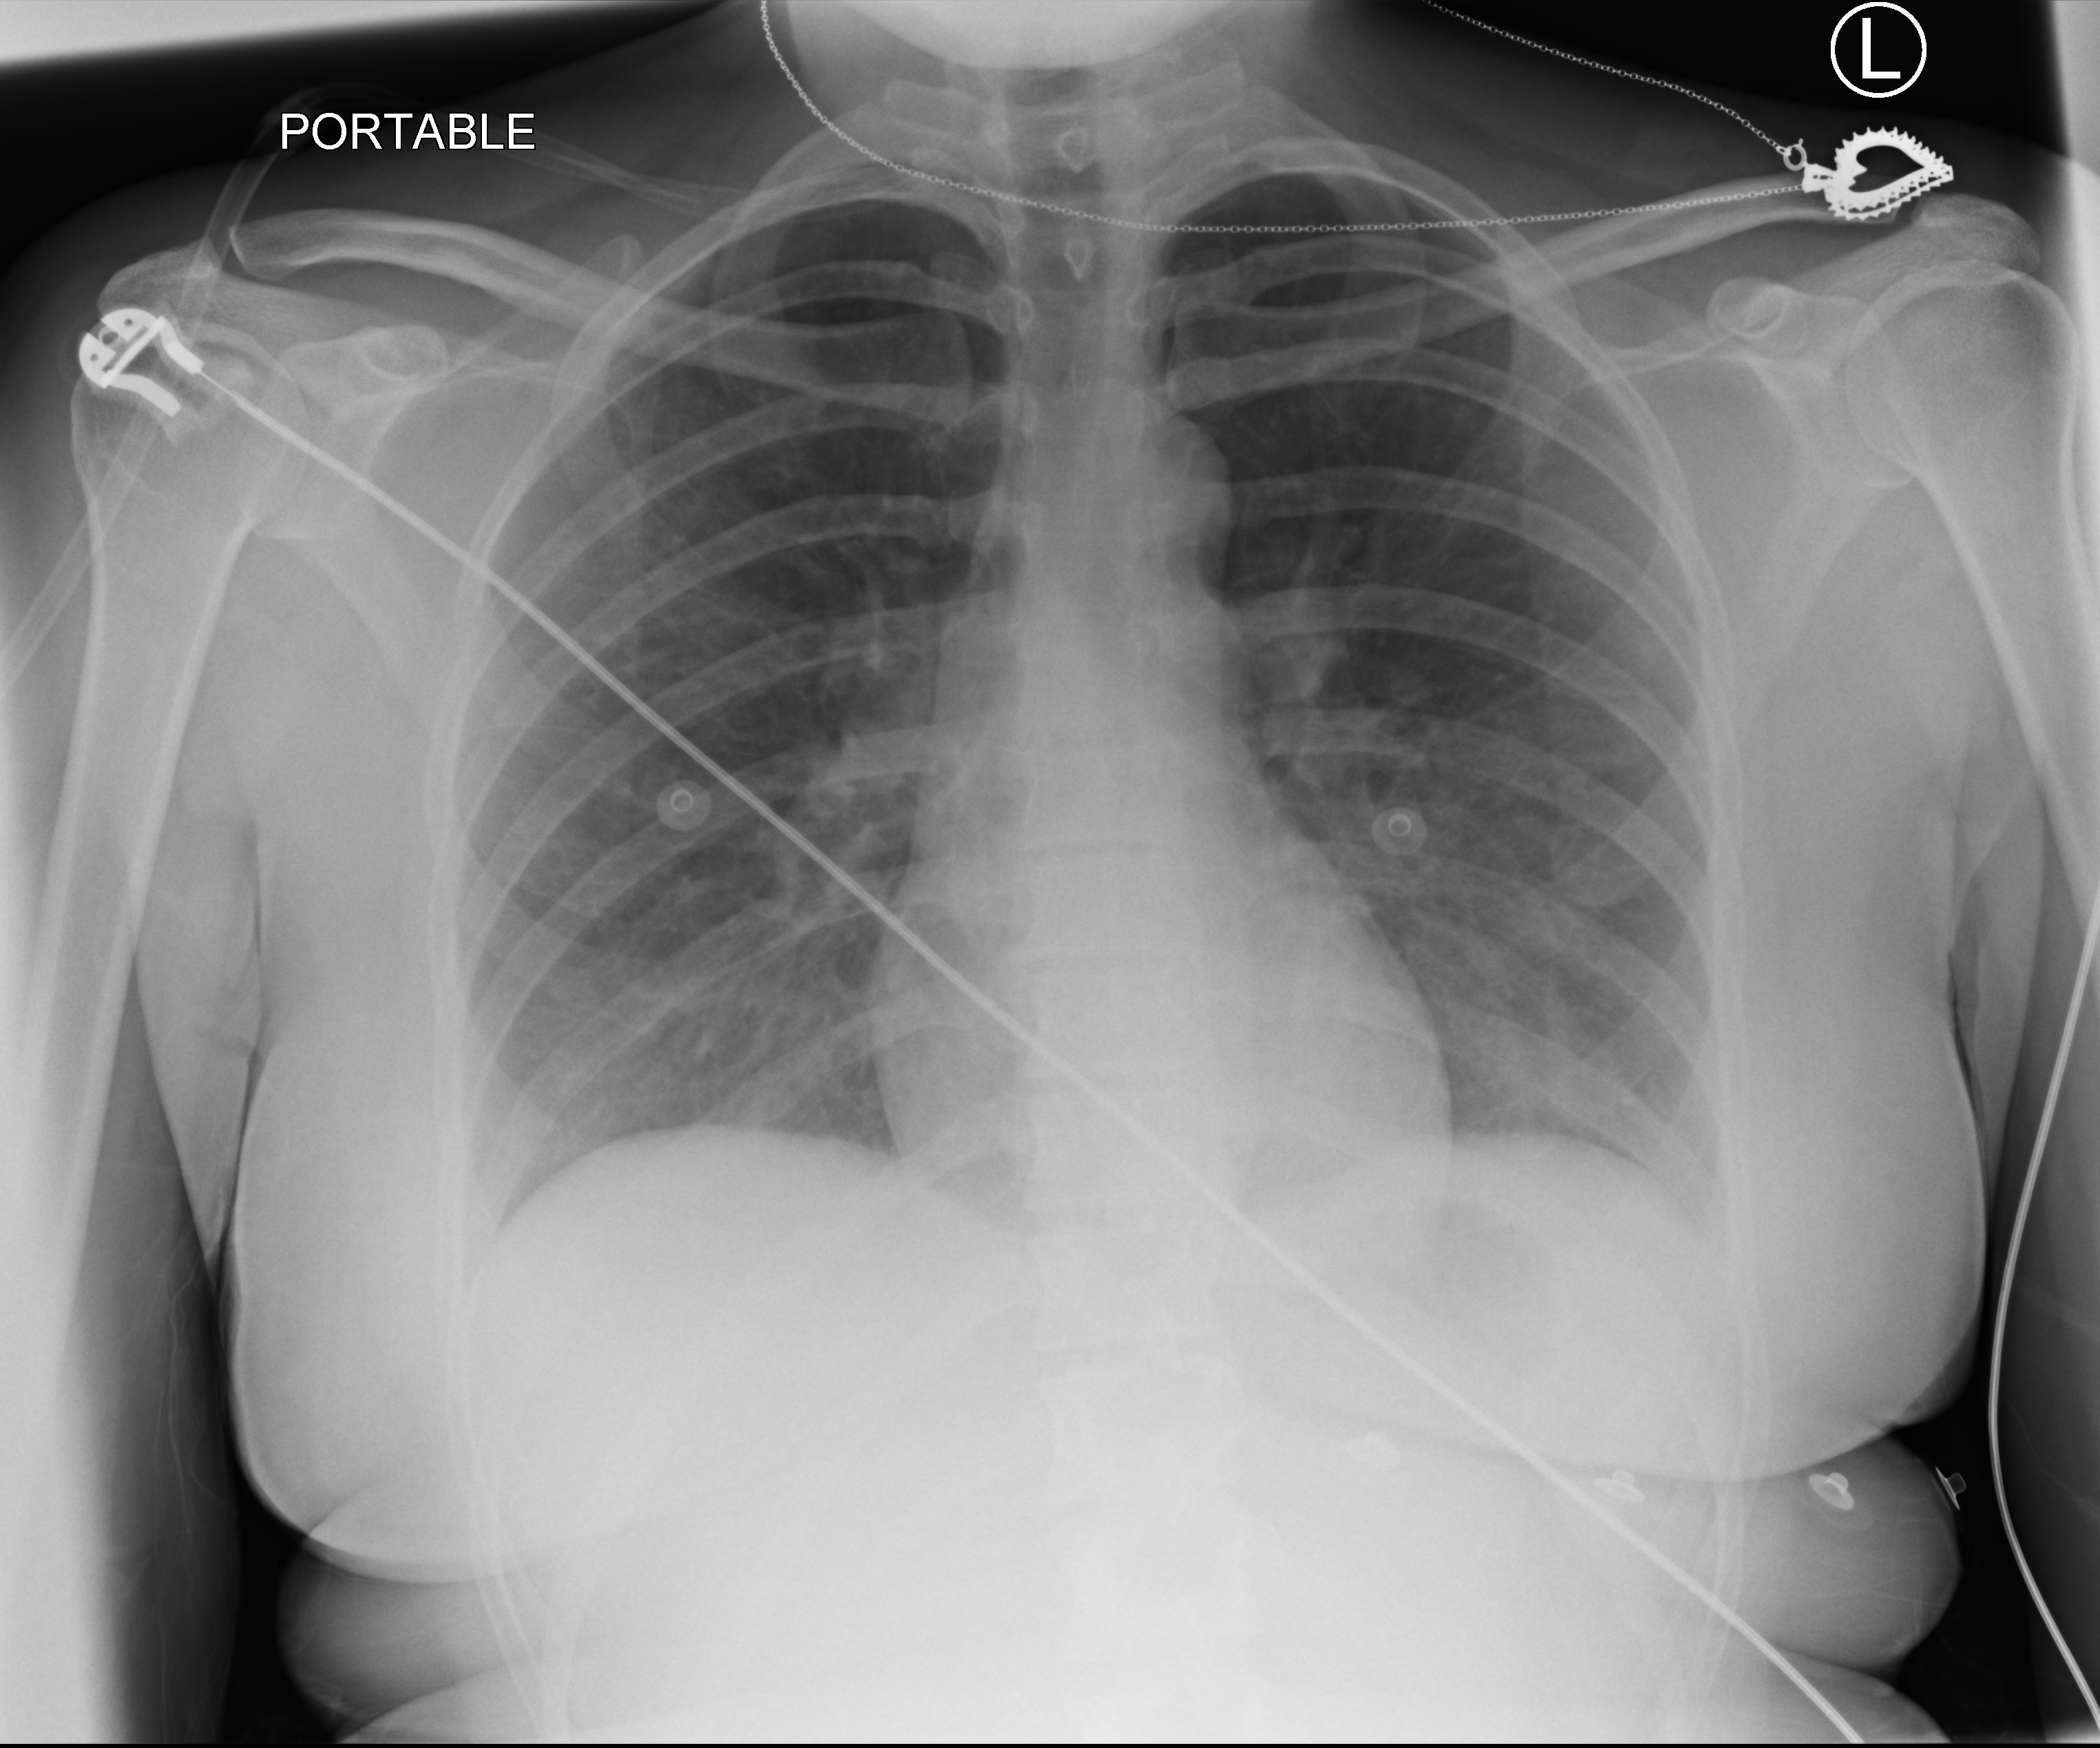
Bedside chest radiograph (computed radiography), anteroposterior (AP) projection. Female patient hospitalised with COVID-19, age 18–59 years.
Hospital-stay facts (about this admission, not read from this image; timing relative to this image not recorded):
- admitted to intensive care during this hospital stay: no